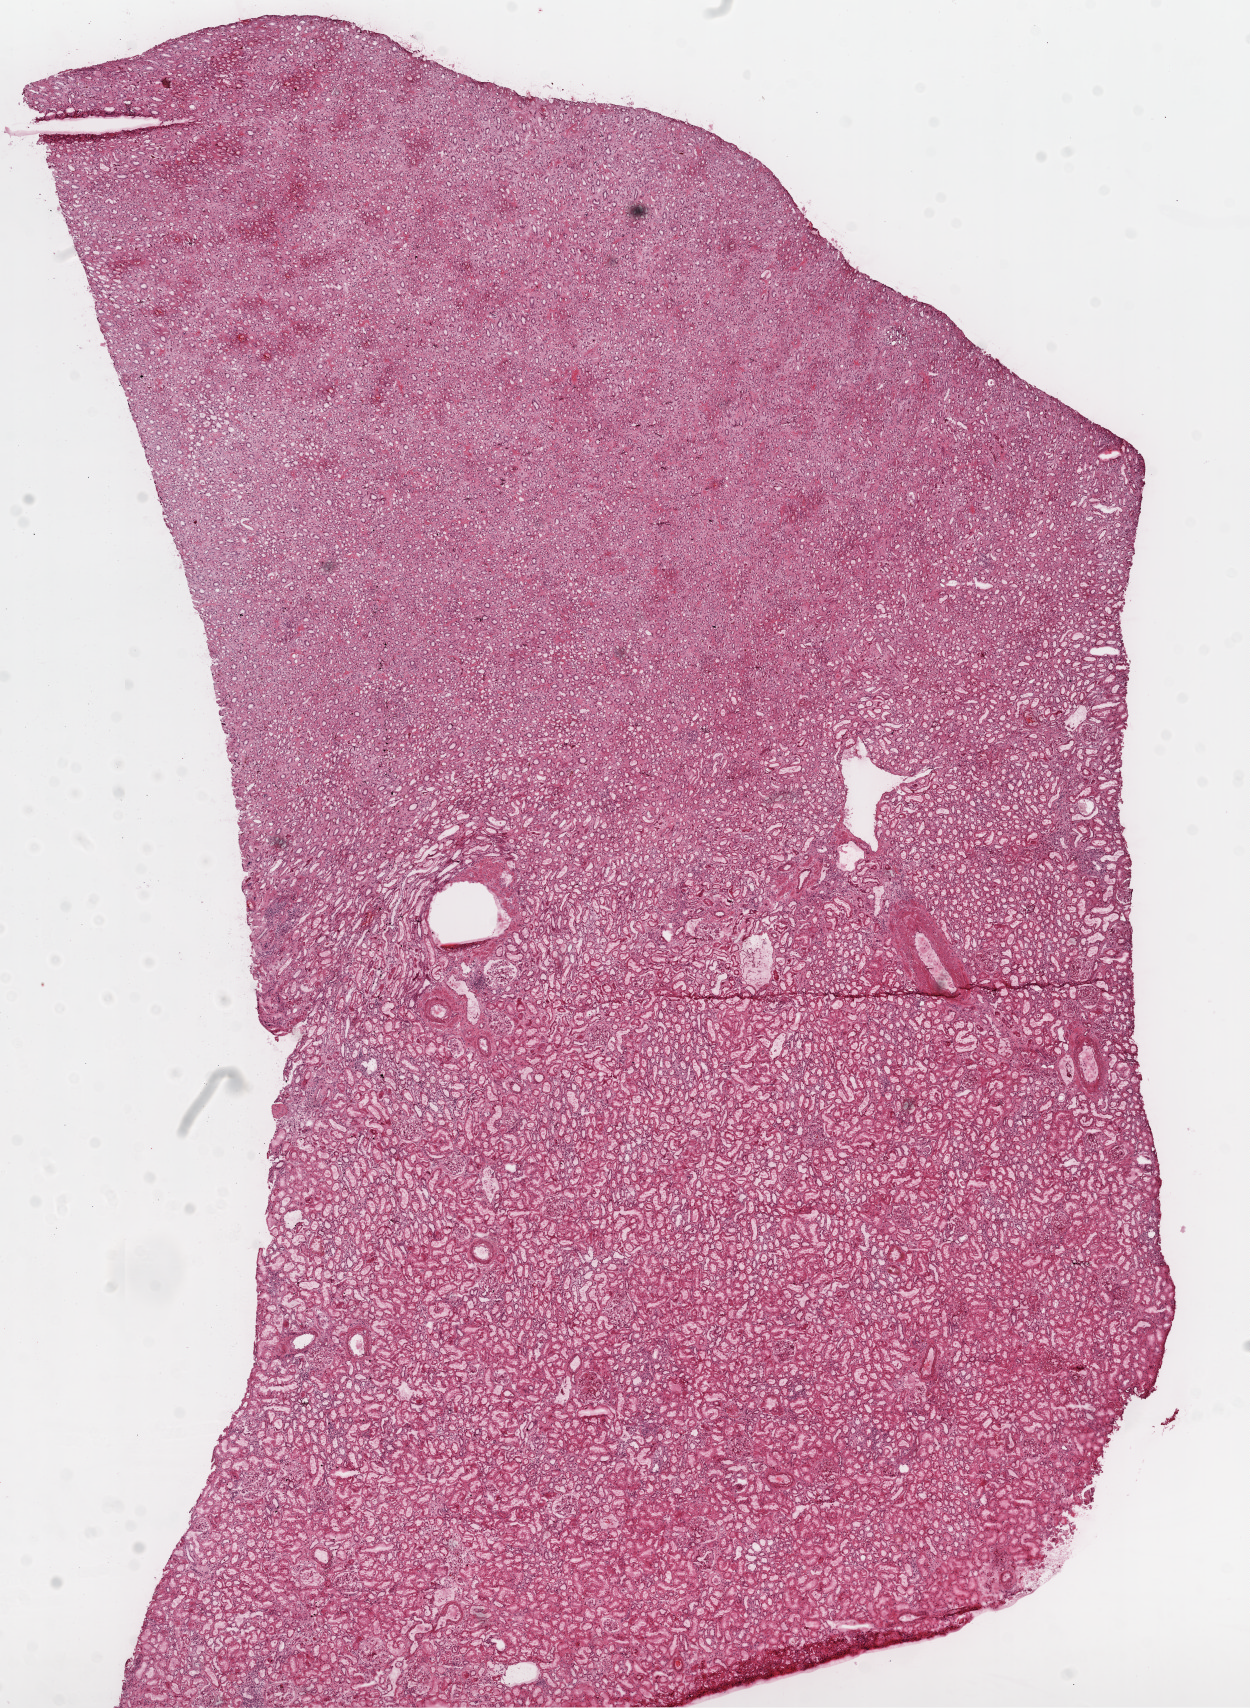
H&E-stained whole-slide image, shown as a low-resolution overview of the whole scanned area (about 10.0 x 13.7 mm), frozen section from the top of the tissue portion, solid tissue normal (non-tumour tissue) sample from the kidney. Patient: male, age at initial diagnosis 74 years.
This section: solid tissue normal sample (biorepository sample class). Patient diagnosis: Clear cell adenocarcinoma, NOS.